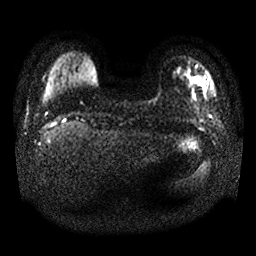
Breast MRI, one axial slice; slice 2 of 25 in the series (ordered by position); diffusion-weighted series; image 2 of 4 stored at this slice position (different b-values; order by instance number); 1.5 T; 4 mm slice thickness; 256 × 256 image matrix, field of view 340 × 340 mm. Female patient.
Annotated regions visible in this slice (manually delineated by an expert):
- tumour on diffusion-weighted imaging: bounding box <189,74,206,91> (left, top, right, bottom; pixels)